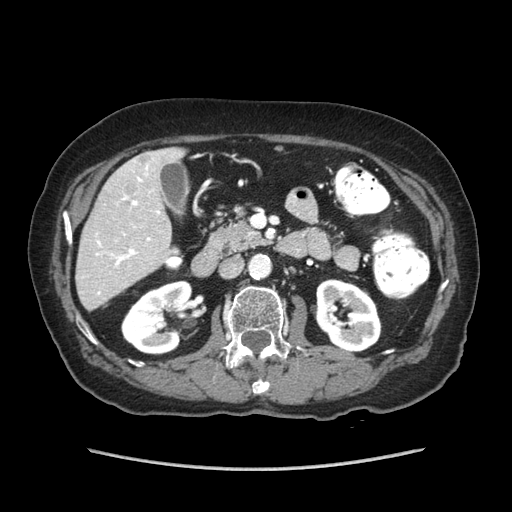
Contrast-enhanced abdominal CT (liver protocol), one axial slice. Position 27 of 89 along the scan axis. Reconstruction kernel STANDARD. Soft-tissue window (W 400 / L 40 HU). 512 × 512 image matrix, field of view 360 × 360 mm. Case-level facts recorded for this patient, not image findings: diagnosis: hepatocellular carcinoma (patient treated with transarterial chemoembolisation; whether this scan precedes or follows treatment is not stated here); TNM stage (as recorded): Stage-IIIA; Child-Pugh class: A; tumour differentiation: well differentiated; tumour nodularity: multinodular.
Structures marked on this image (semi-automatically segmented with operator editing):
- liver parenchyma outside the tumour (the mass and vessels are separate outlines, so this box may not span the whole liver): bounding box (x1, y1, x2, y2) in pixels: (76, 148, 184, 310)
- mass: (109, 152, 159, 200)
- liver vessels: (96, 164, 160, 294)